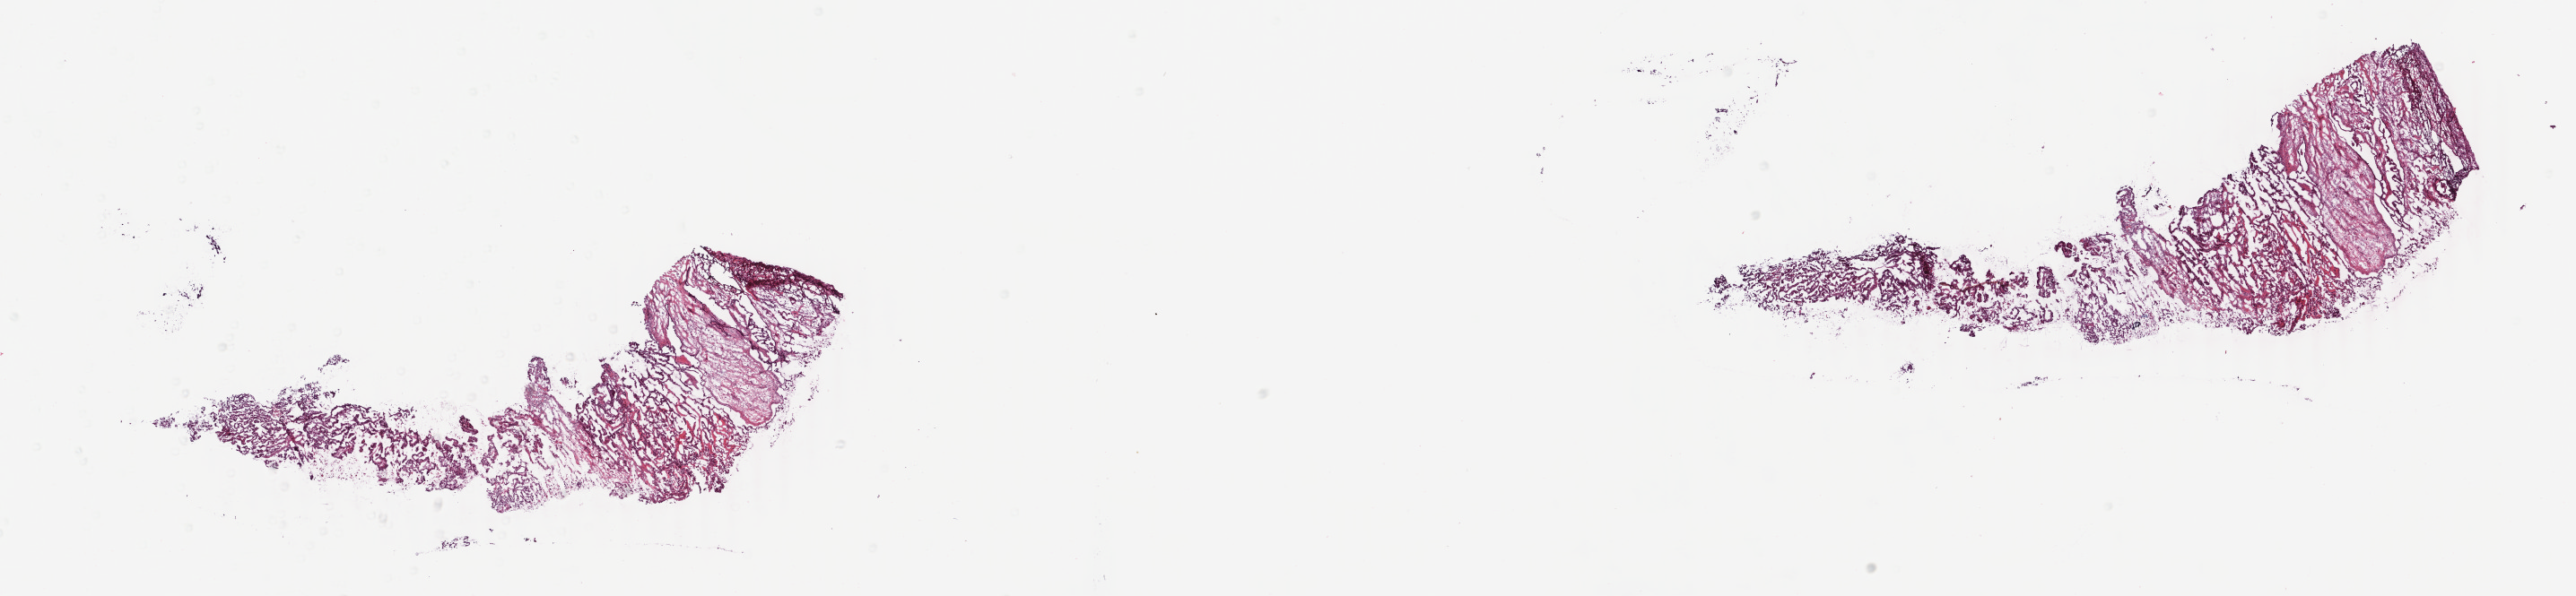
H&E-stained whole-slide image, whole scanned area (about 22.8 x 5.3 mm) shown as a low-resolution overview; frozen section; sample: primary tumour, uterus. Female, age 82 years at initial diagnosis. Histologic grade: G2 (moderately differentiated). Composition of this section per pathologist review: tumour cells 50%, tumour nuclei 60%, normal cells 30%, stromal cells 10%, necrosis 10%. Inflammatory infiltration, as recorded: lymphocyte infiltration 1%, monocyte infiltration 0%, neutrophil infiltration 0%.
* histologic diagnosis: Endometrioid adenocarcinoma, NOS (endometrium)
* FIGO stage: IIIA